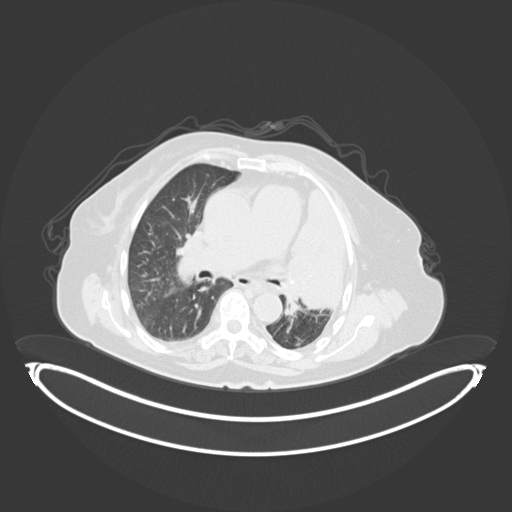
Chest CT, one axial slice. Position 202 of 284 along the scan axis. 120 kVp. Lung window (W 1500 / L -600 HU). 512 × 512 image matrix. Patient: female, 75 years. Case-level facts recorded for this patient, not image findings: clinical TNM (as recorded): T3 N3 M1.
Outlined on this slice (rectangle marked by the reading radiologist):
- lung tumour (recorded histology: adenocarcinoma): bounding box (x1, y1, x2, y2) in pixels: (283, 179, 358, 319)